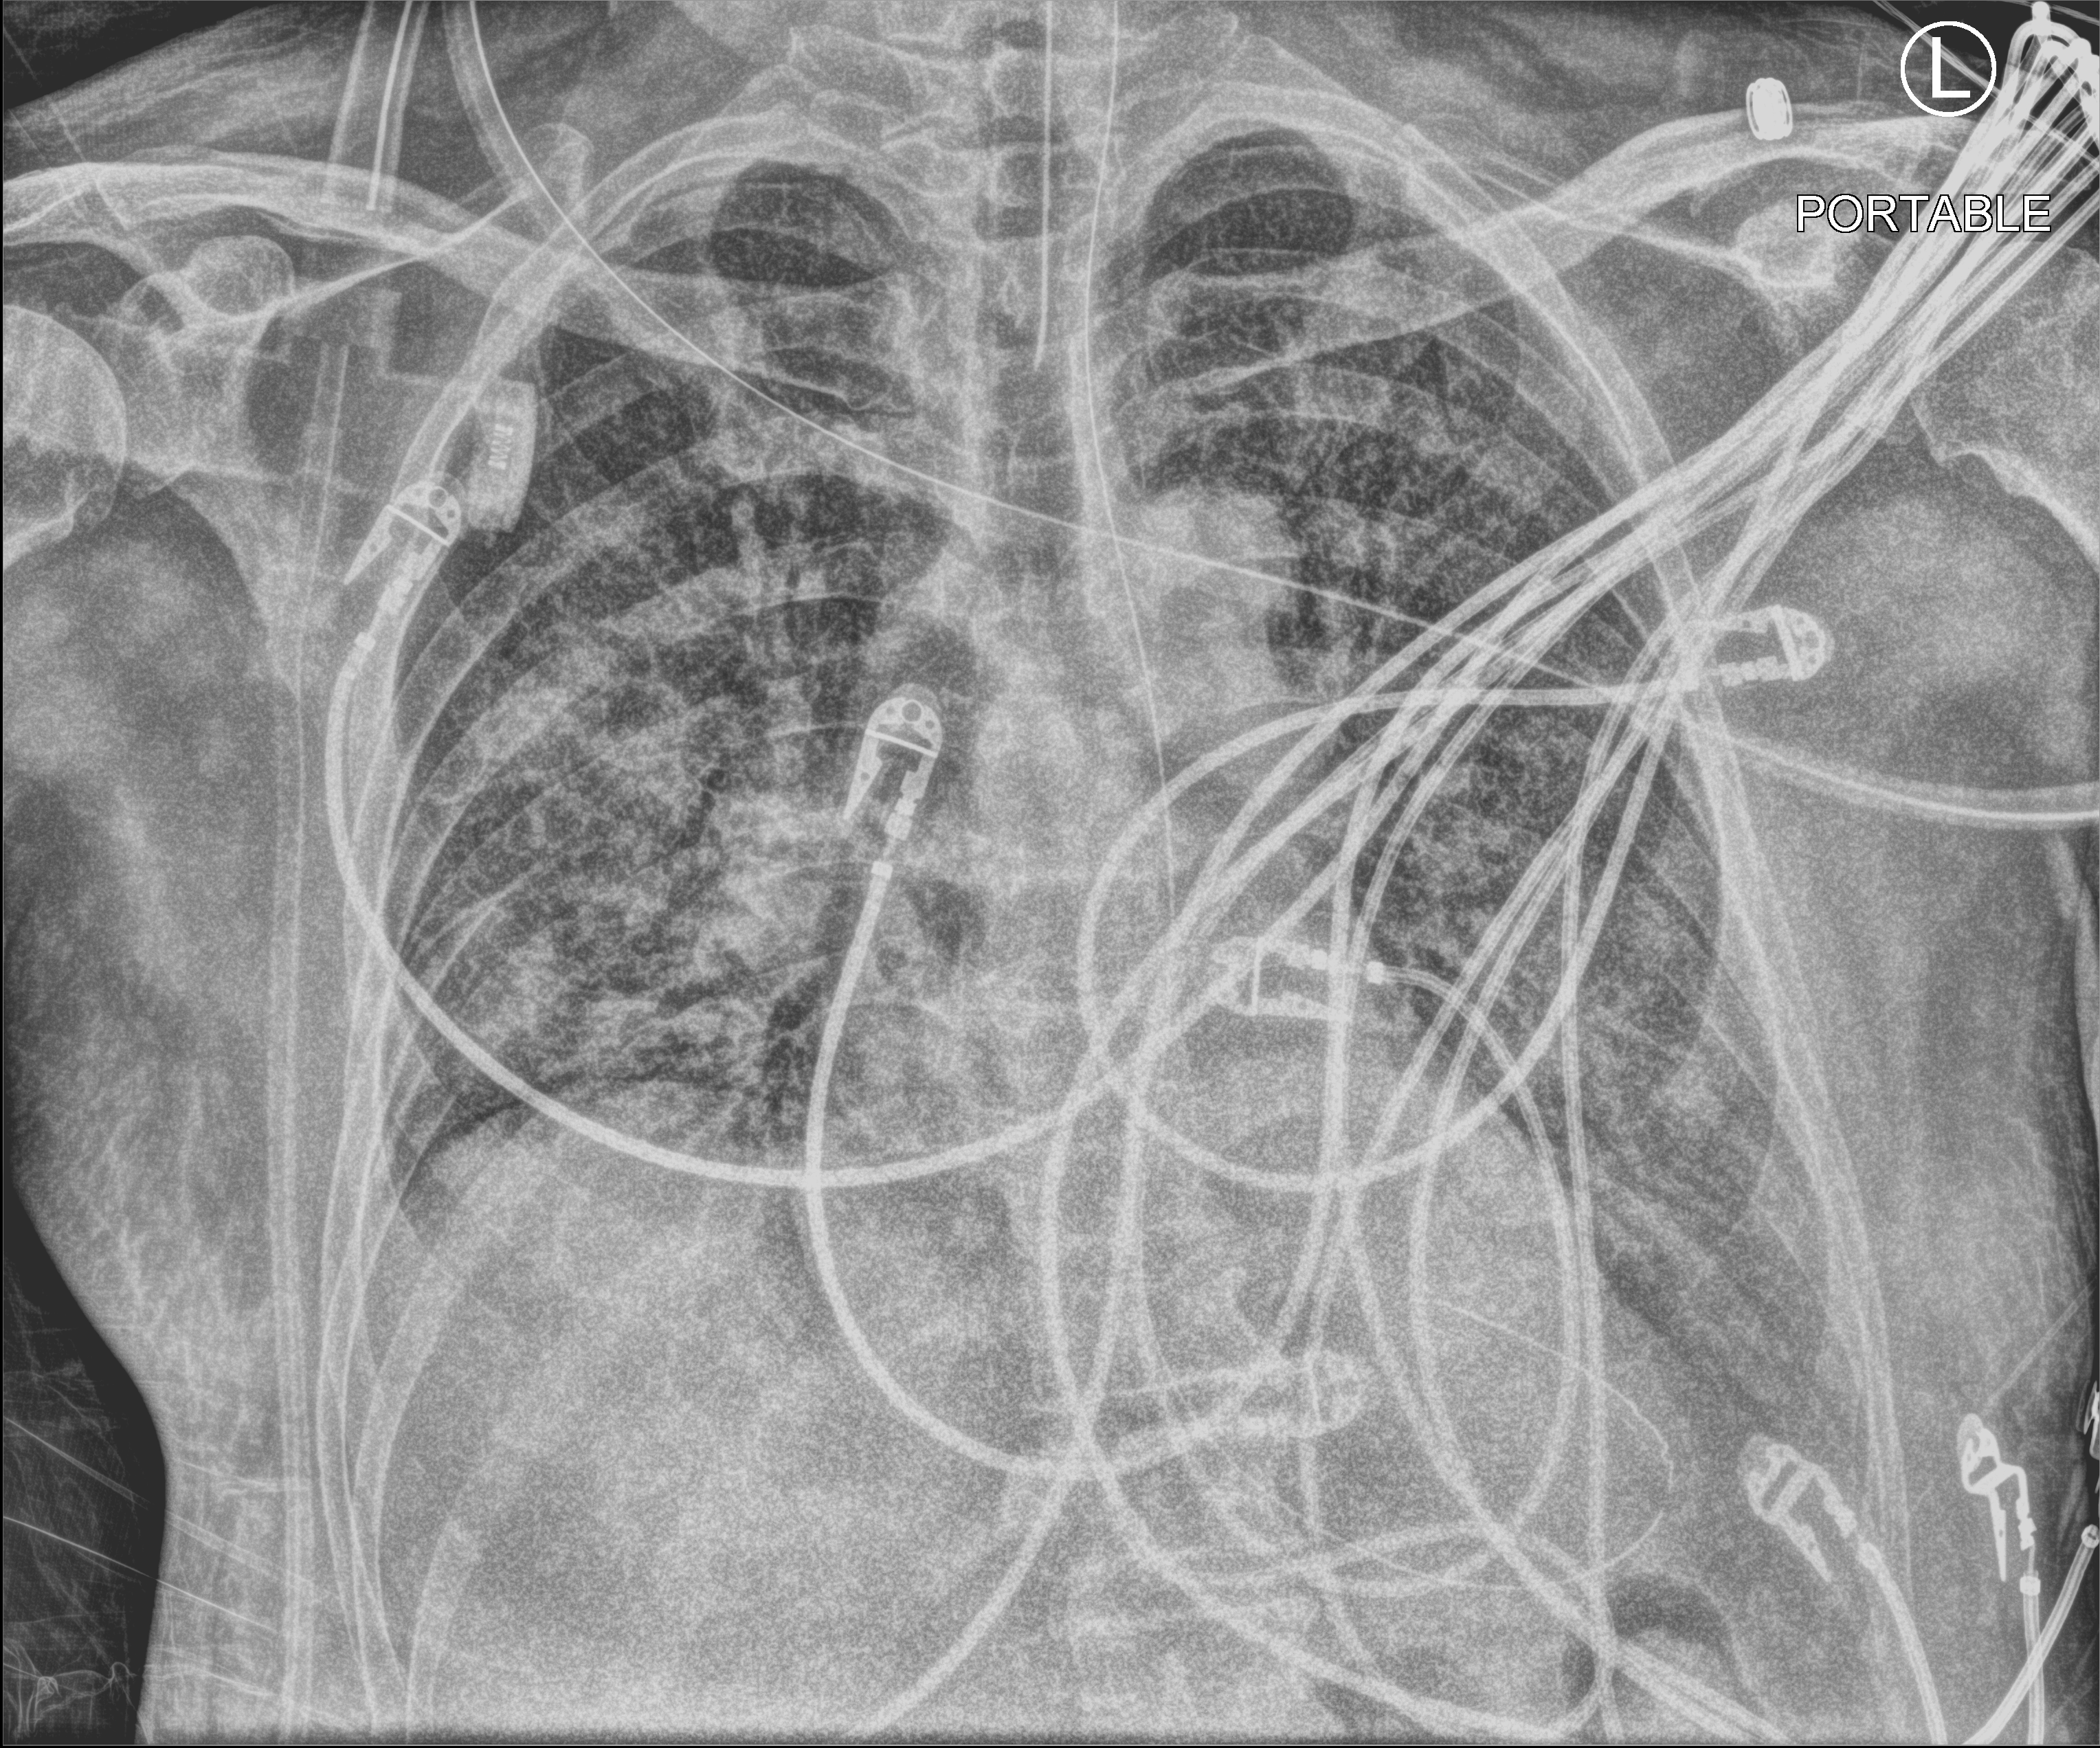
Portable chest radiograph; anteroposterior (AP) projection. Male patient hospitalised with COVID-19, age 60–74 years.
Hospital-stay facts (about this admission, not read from this image; timing relative to this image not recorded): smoking status (admission record): former; chronic kidney disease (admission record): no; admitted to intensive care during this hospital stay: yes.